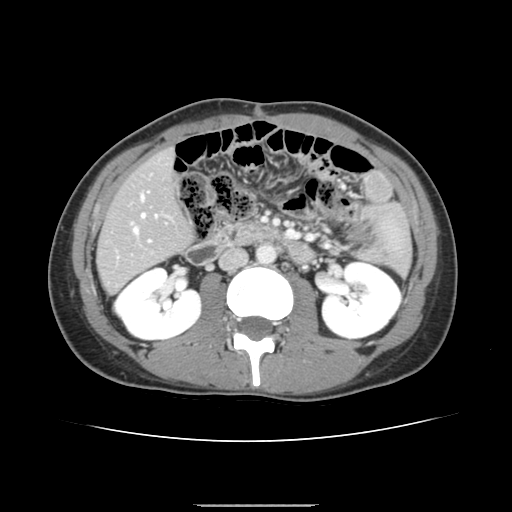
Contrast-enhanced abdominal CT, one axial slice. Slice 60 of 150 in the series (ordered by position). Soft-tissue window (W 400 / L 40 HU). 2.5 mm slice thickness. 512 × 512 image matrix, field of view 324 × 324 mm. Female patient, age 32 years. Case-level facts recorded for this patient, not image findings: diagnosis: colorectal cancer liver metastases, imaged before liver resection; multiple liver metastases: yes; largest metastasis: 0.7 cm; disease in both lobes: no.
Structures marked on this image (manually delineated by an expert):
- hepatic veins: box from (x=134, y=195) to (x=157, y=233) px
- liver: (x=98, y=150)–(x=191, y=292)
- planned liver remnant (the part of the liver to remain after resection): (x=98, y=150)–(x=191, y=292)
- portal vein (with intrahepatic branches): (x=131, y=191)–(x=151, y=242)